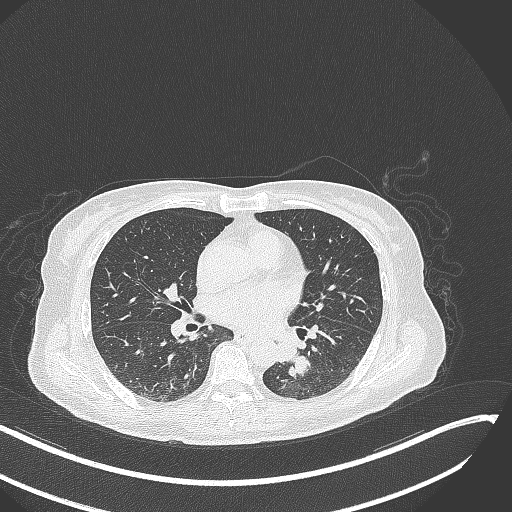
Chest CT, one axial slice; slice 130 of 342 in the series (ordered by position); reconstruction kernel B70f; 120 kVp; lung window (W 1500 / L -600 HU); 1 mm slice thickness; 512 × 512 image matrix. Female patient, age 64 years. Case-level facts recorded for this patient, not image findings: clinical TNM (as recorded): T3 N1 M1.
Structures marked on this image (rectangle marked by the reading radiologist):
- lung tumour (recorded histology: small cell carcinoma): box from (x=271, y=332) to (x=314, y=385) px